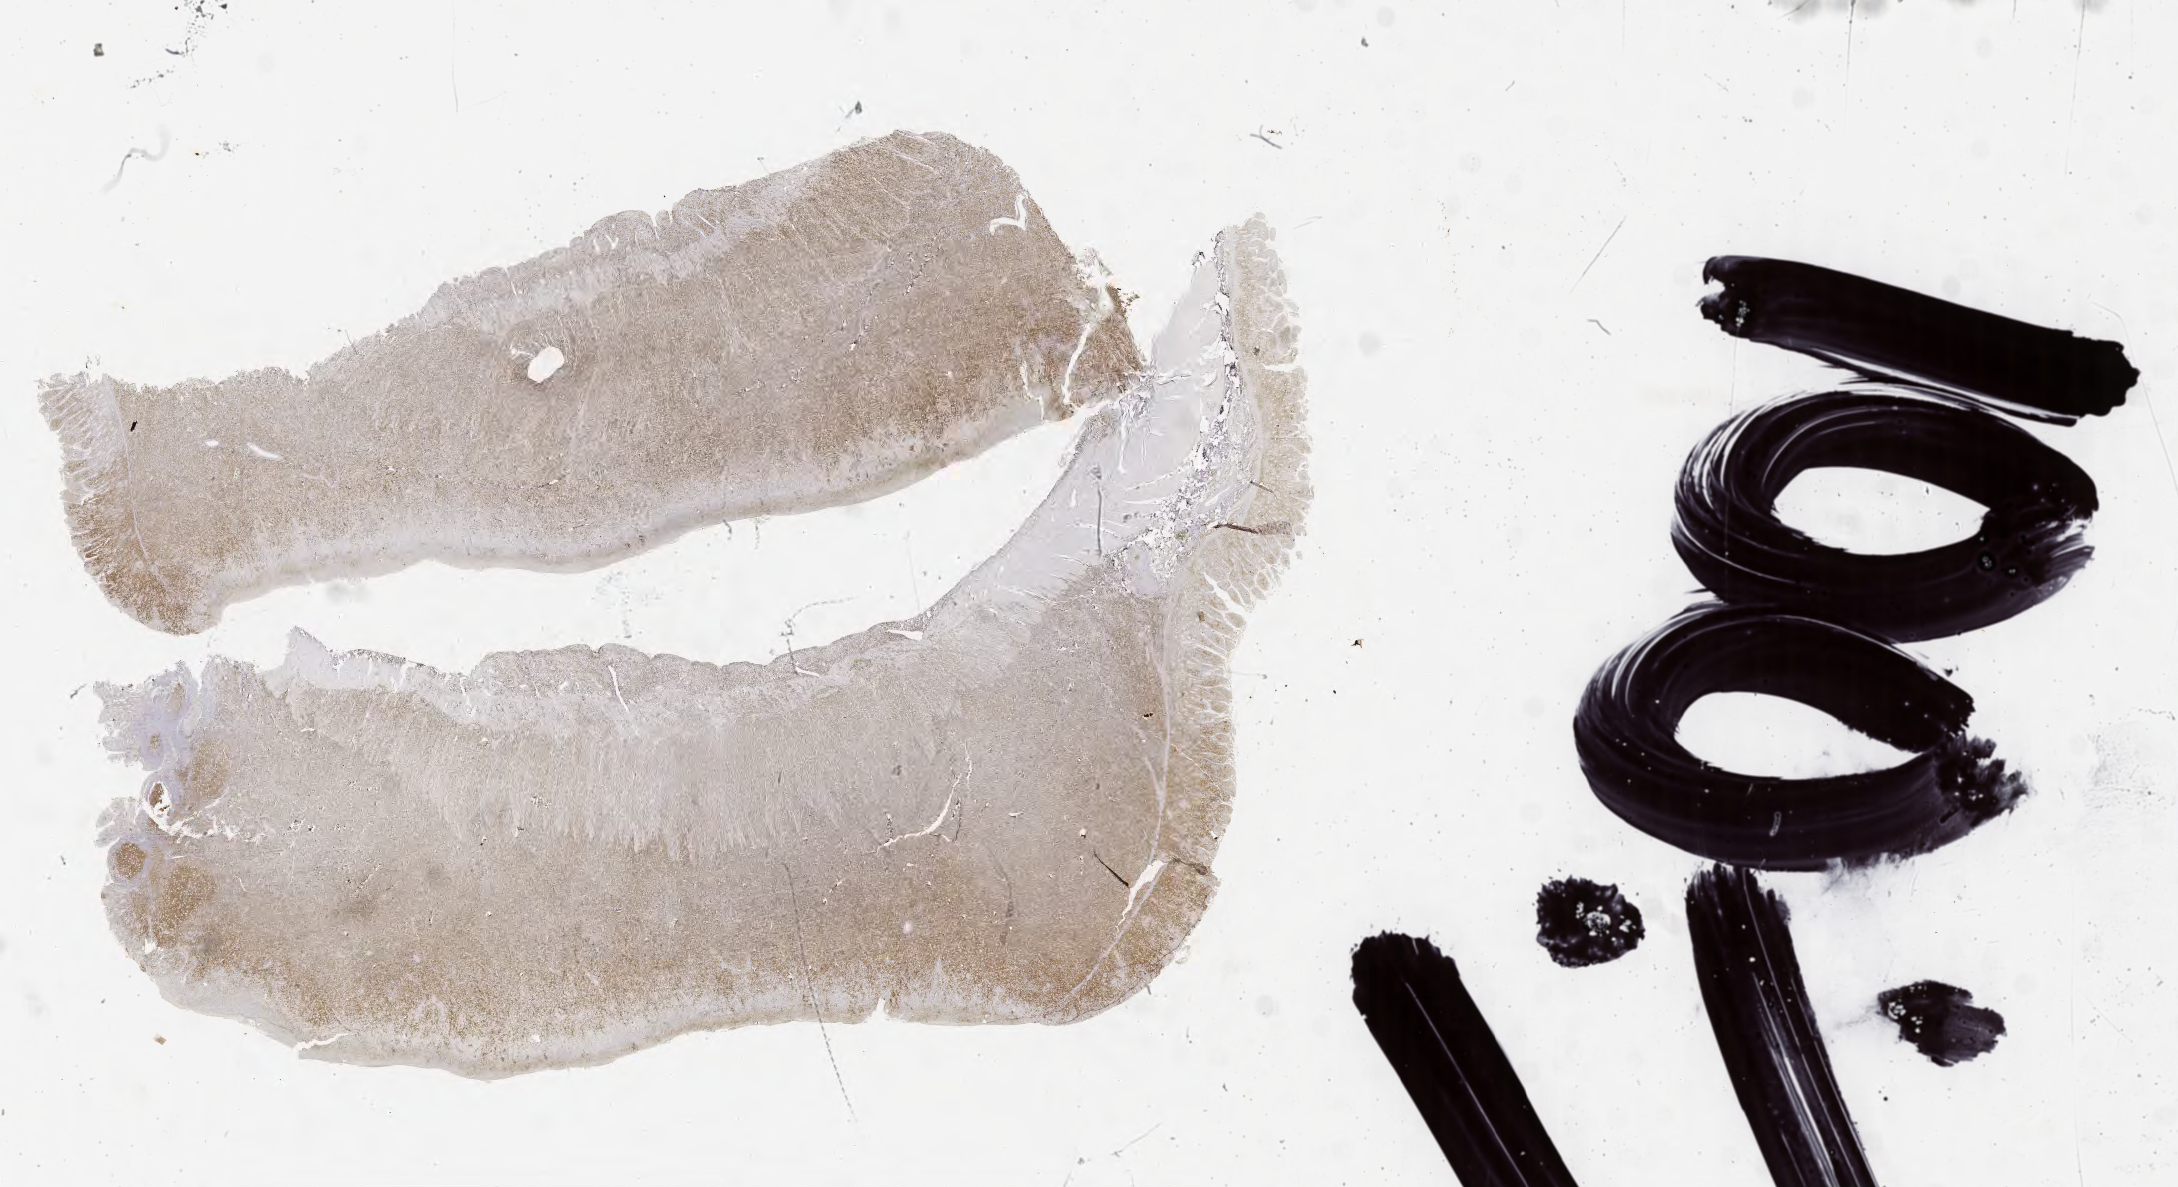
Whole-slide image, immunohistochemical stain for Ki-67, whole scanned area (about 35.2 x 19.2 mm) shown as a low-resolution overview. Tumor tissue. Female patient, age 27 years.
Histologic diagnosis: Burkitt lymphoma, NOS.